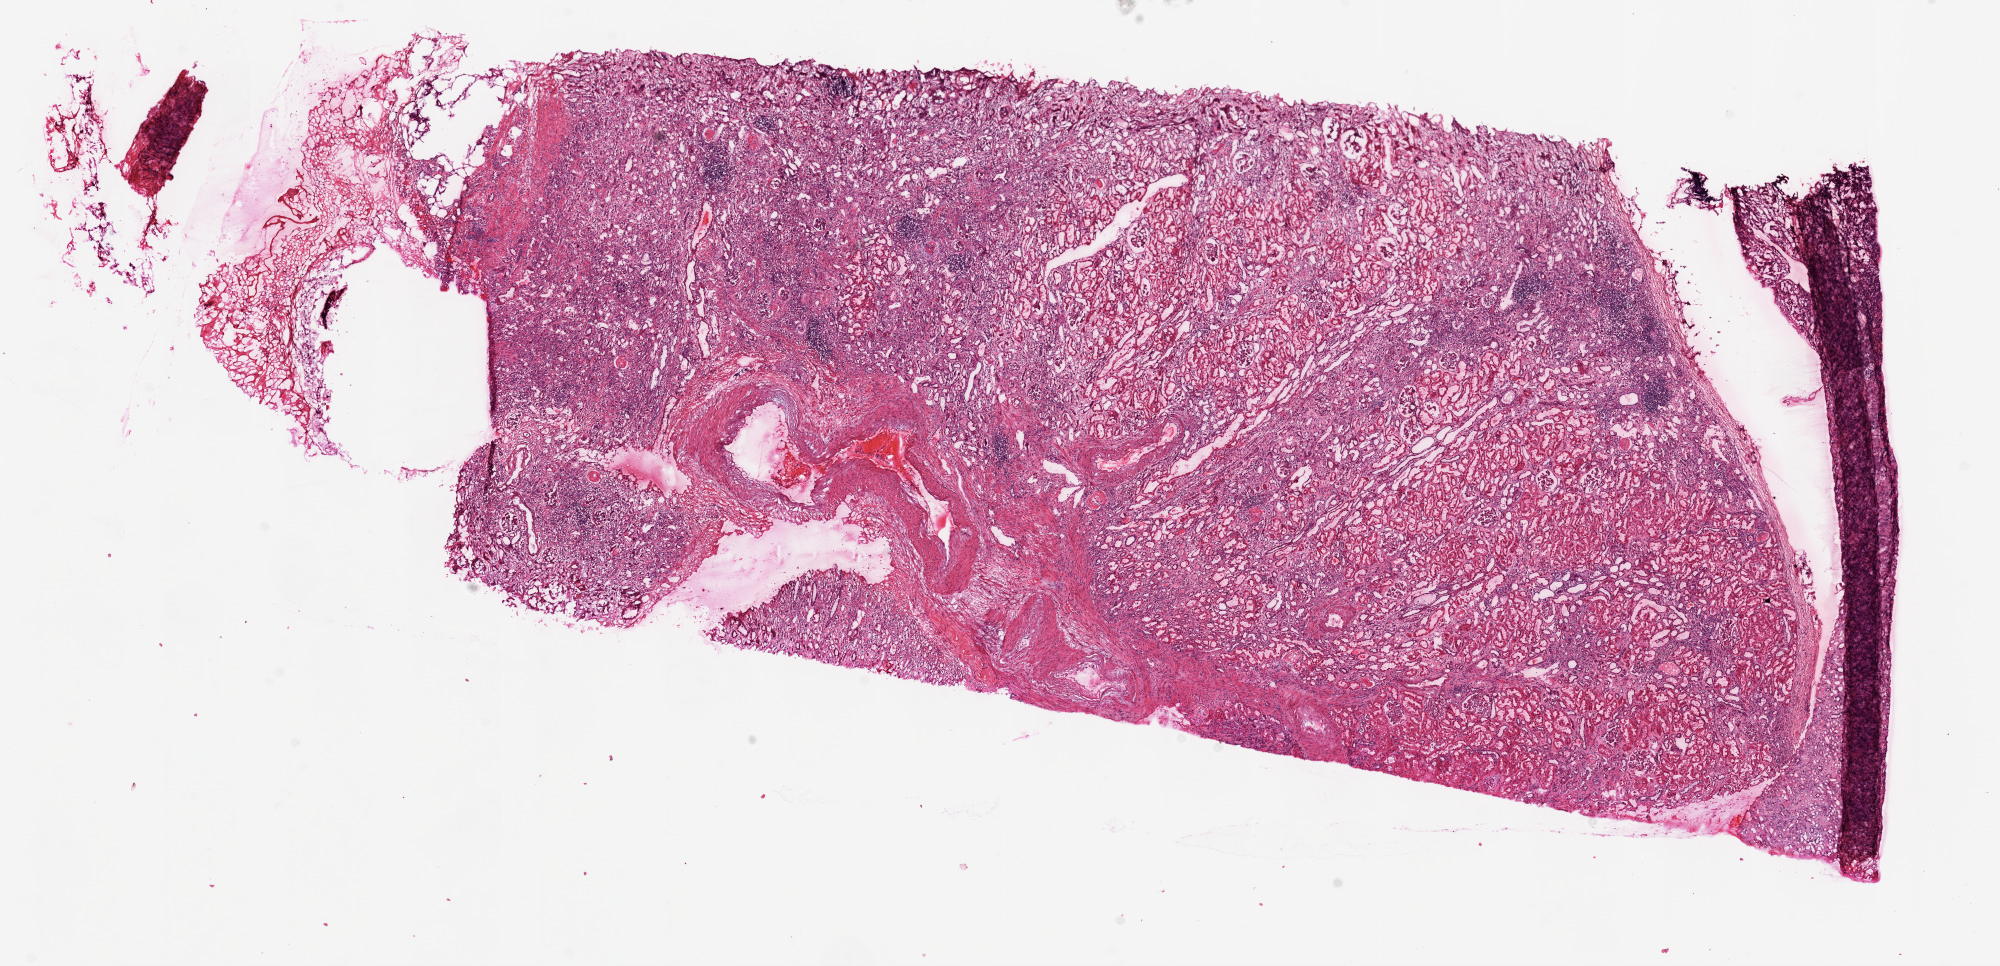
H&E-stained whole-slide image, shown as a low-resolution overview of the whole scanned area (about 16.0 x 7.8 mm); frozen section; kidney, solid tissue normal (non-tumour tissue) sample. Patient: female, age at initial diagnosis 69 years.
This section: solid tissue normal (non-tumour) sample from the same patient. Patient diagnosis: Clear cell adenocarcinoma, NOS.